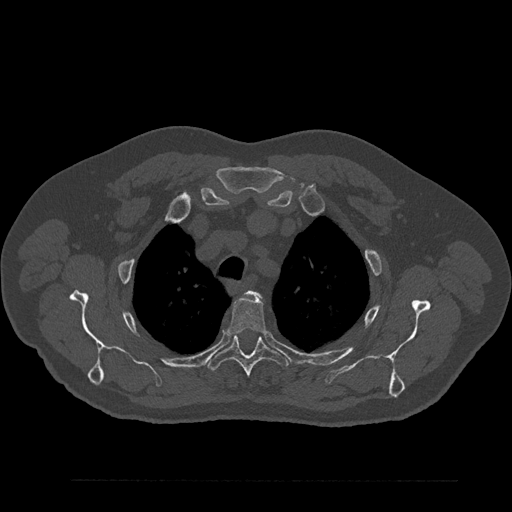
CT including the spine, one axial slice; position 663 of 797 along the scan axis; reconstruction kernel Br40s/3; 120 kVp; bone window (W 1800 / L 400 HU); 0.5 mm slice thickness; 512 × 512 image matrix, field of view 430 × 430 mm. Patient: male, 61 years. Case-level facts recorded for this patient, not image findings: primary cancer: prostate.
Structures marked on this image (semi-automatic segmentation, software-assisted and operator-edited):
- T2 vertebra: bounding box [x1, y1, x2, y2] px = [247, 291, 260, 297]
- T3 vertebra: [228, 297, 267, 335]
- T4 vertebra: [207, 335, 288, 378]